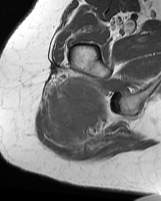
MRI of an extremity soft-tissue mass, one axial slice. Position 43 of 70 along the scan axis. MR volume resampled by the dataset authors to the PET/CT grid (not the native acquisition matrix). 3.27 mm slice thickness. 161 × 201 image matrix. Female patient. Case-level facts recorded for this patient, not image findings: histological type: synovial sarcoma; grade: intermediate; site of the primary tumour: right buttock.
Structures marked on this image (expert contour drawn on MRI and transferred to this co-registered scan by the dataset authors):
- gross tumour volume including surrounding oedema: box from (x=49, y=77) to (x=111, y=155) px
- gross tumour volume (mass): (x=49, y=77)–(x=107, y=142)